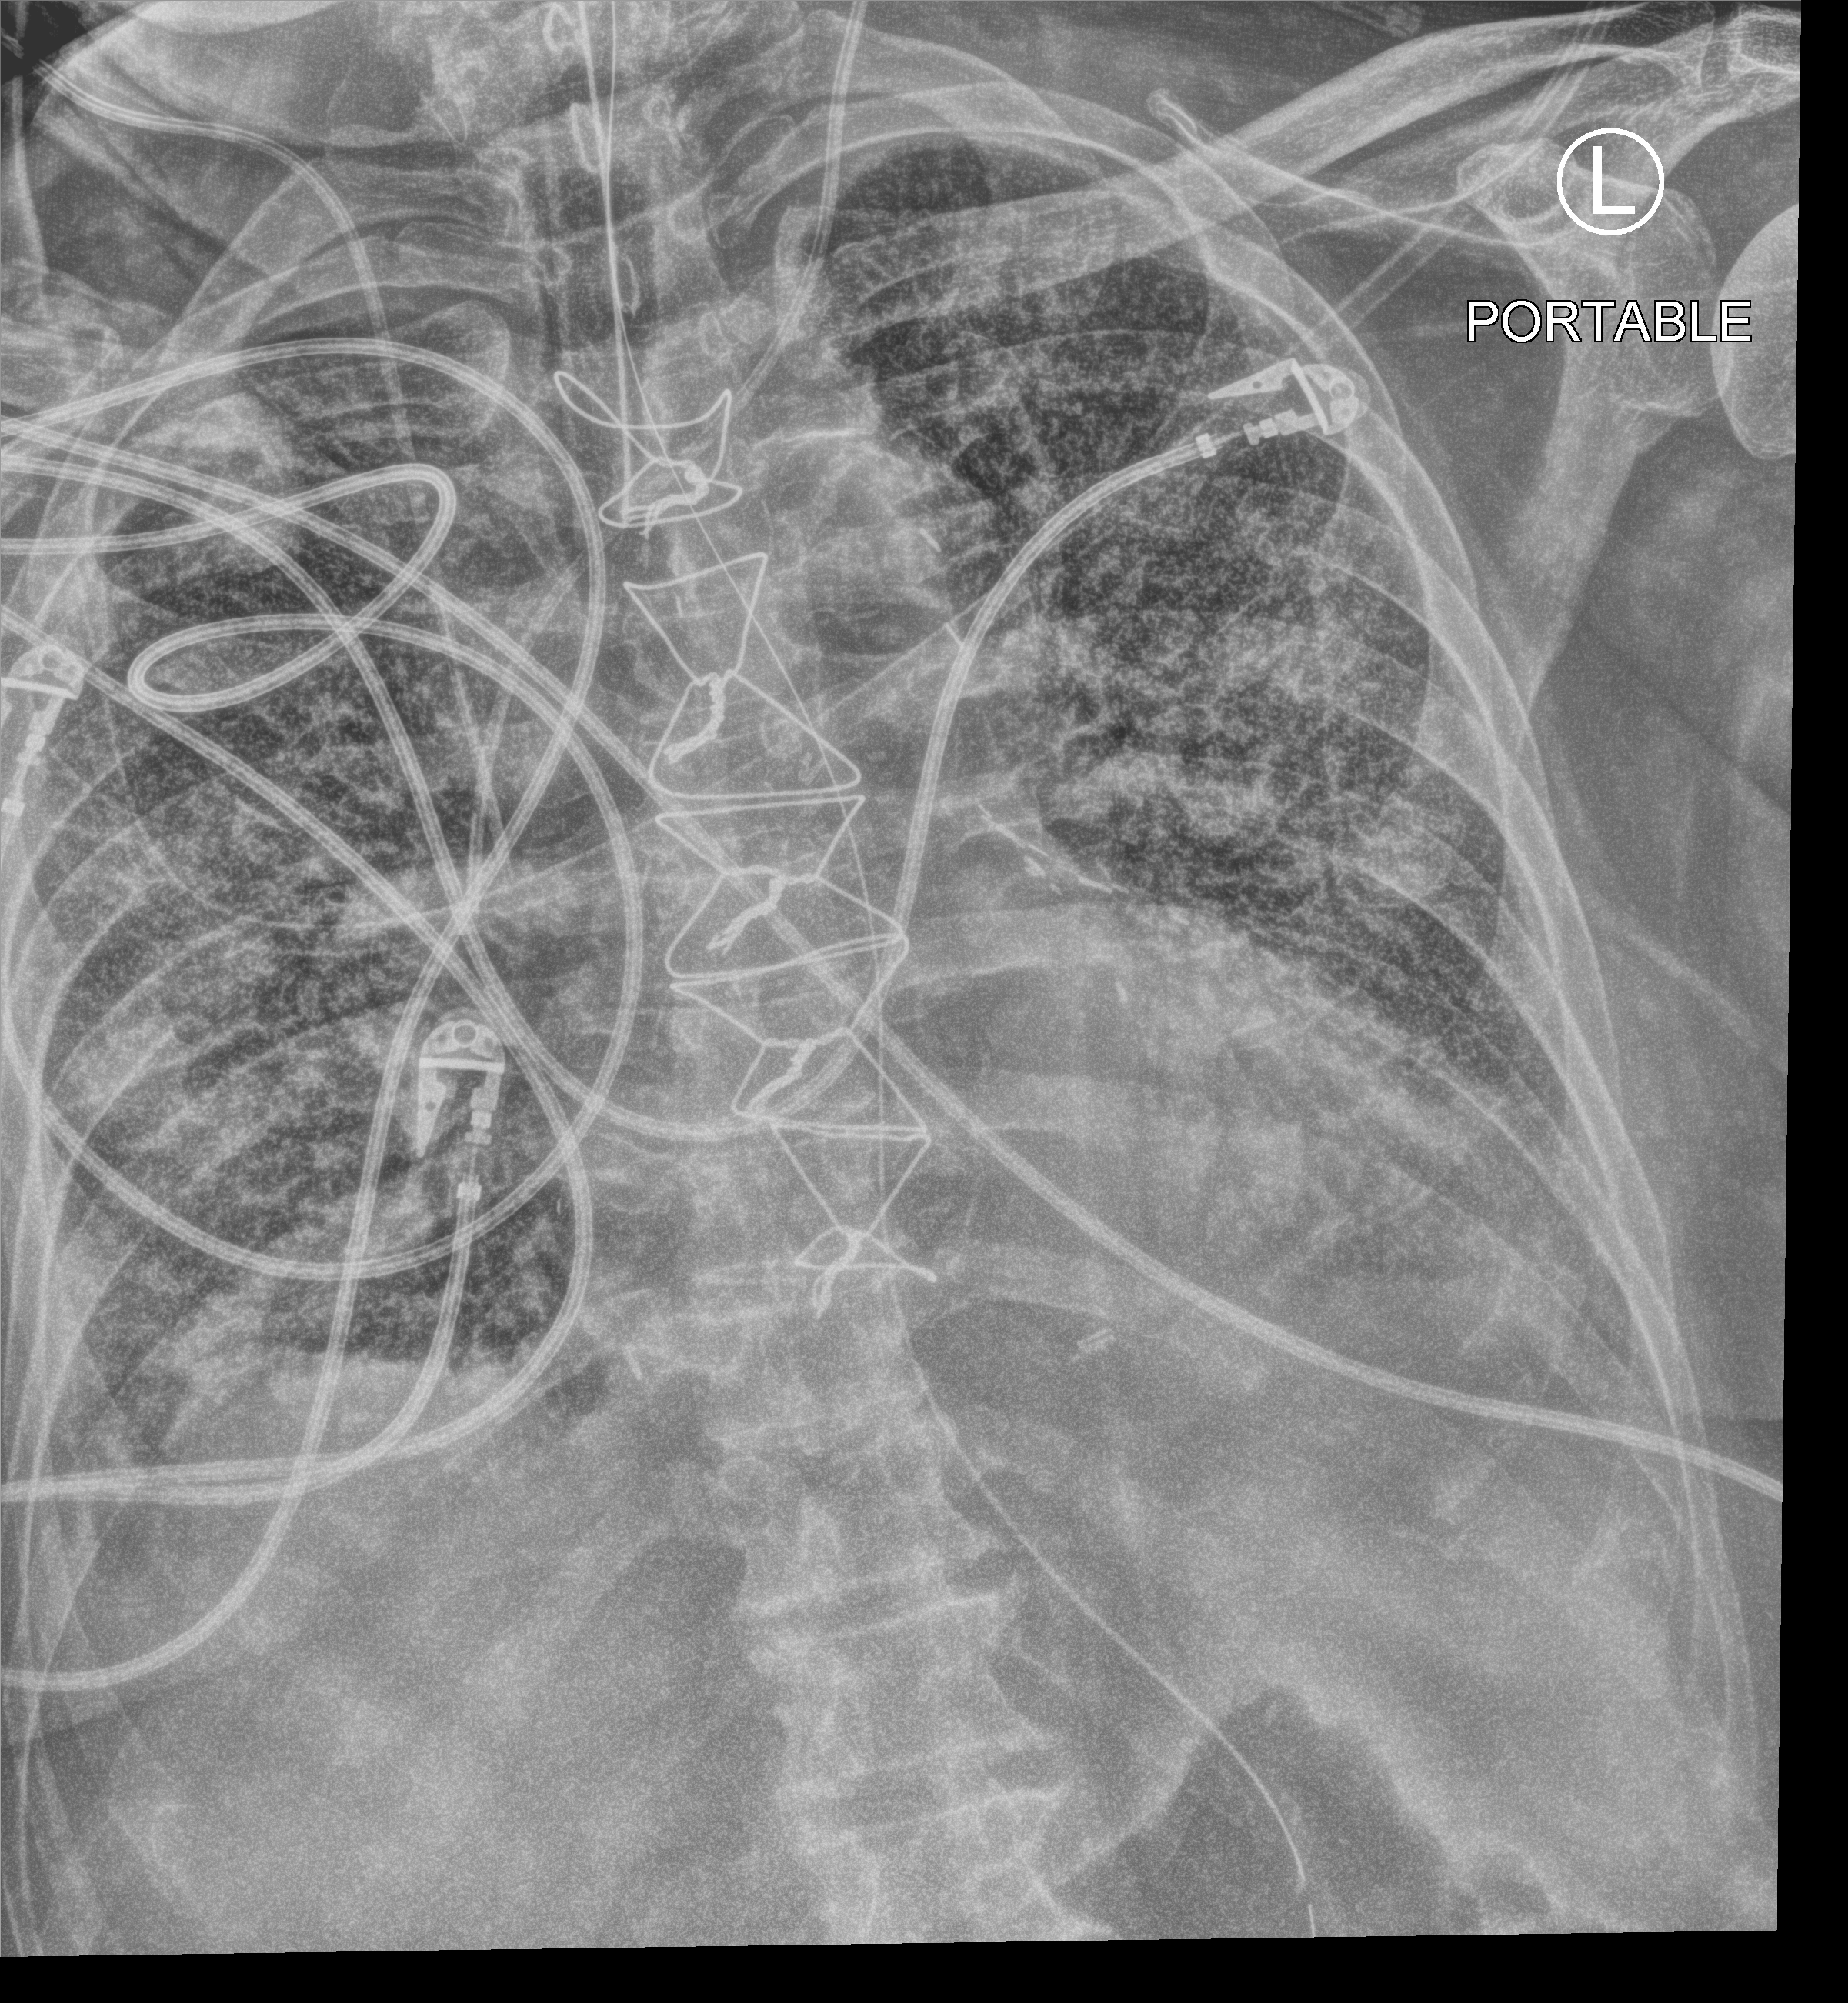
Bedside chest radiograph (computed radiography); anteroposterior (AP) projection. Patient hospitalised with COVID-19; male, aged 75–90 years.
Hospital-stay facts (about this admission, not read from this image; timing relative to this image not recorded):
- other chronic lung disease (admission record): yes
- mechanically ventilated during this hospital stay: yes
- admitted to intensive care during this hospital stay: yes